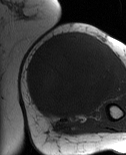
MRI of an extremity soft-tissue mass, one axial slice; position 32 of 86 along the scan axis; MR volume resampled by the dataset authors to the PET/CT grid (not the native acquisition matrix); 126 × 155 image matrix. Female patient. From the clinical record (not read from this slice): histological type: pleiomorphic leiomyosarcoma; grade: high; site of the primary tumour: left biceps.
Structures marked on this image (expert contour drawn on MRI and transferred to this co-registered scan by the dataset authors):
- gross tumour volume including surrounding oedema: box from (x=25, y=33) to (x=115, y=121) px
- gross tumour volume (mass): (x=25, y=33)–(x=115, y=119)